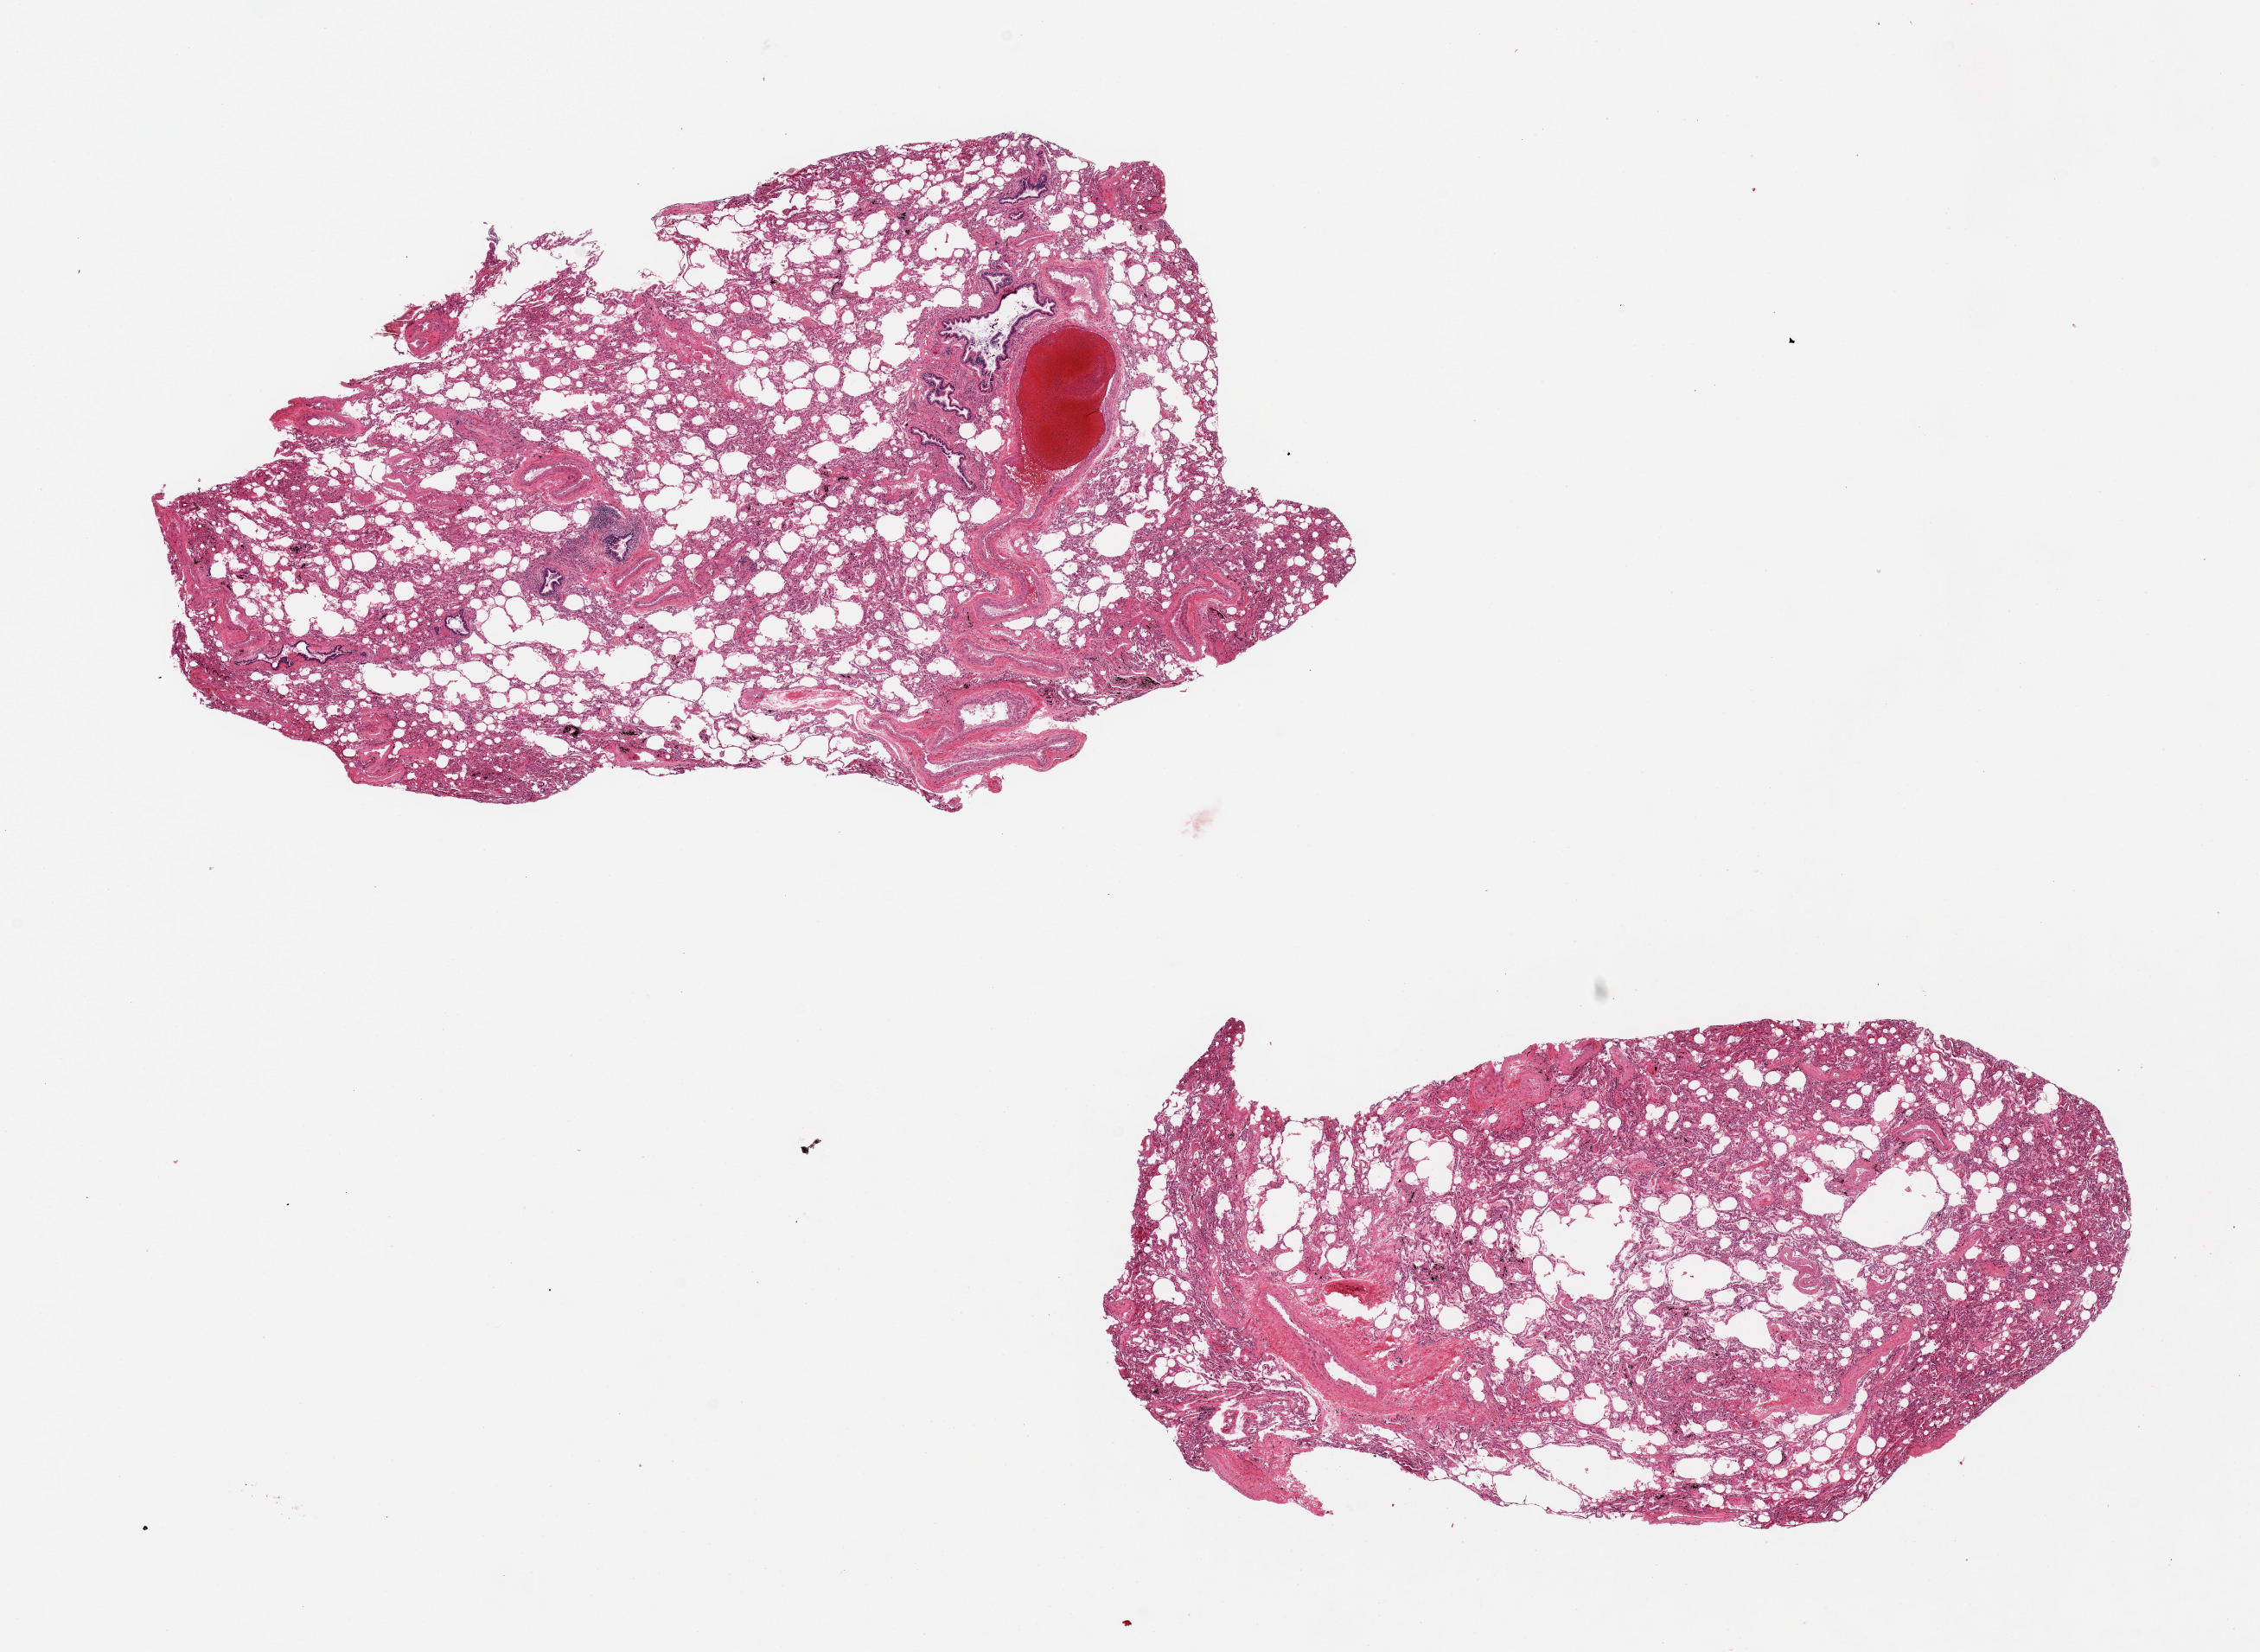
Whole-slide image, hematoxylin and eosin (H&E) stain, a low-resolution overview of the entire scanned area, about 20.7 x 15.1 mm (slide scanned at 20x); PAXgene-fixed paraffin-embedded (PFPE) section; sampled site (target tissue): lung; donor tissue sample. Donor sex: female.
Pathologist's review note for this sample: 2 pieces, 11x6 & 9x5mm; patchy chronic bronciolitis.